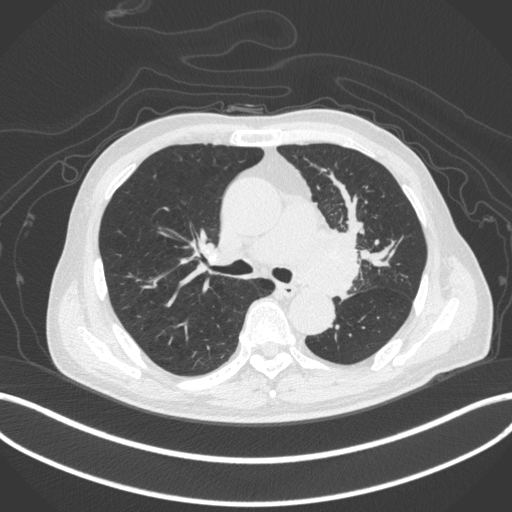
Chest CT, one axial slice; reconstruction kernel B31f; 120 kVp; lung window (W 1500 / L -600 HU); 1 mm slice thickness; 512 × 512 image matrix, field of view 400 × 400 mm. Patient: male, 77 years. From the clinical record (not read from this slice): clinical TNM (as recorded): T3 N1 M0.
Structures marked on this image (rectangle marked by the reading radiologist):
- lung tumour (recorded histology: adenocarcinoma): box from (x=290, y=231) to (x=362, y=300) px